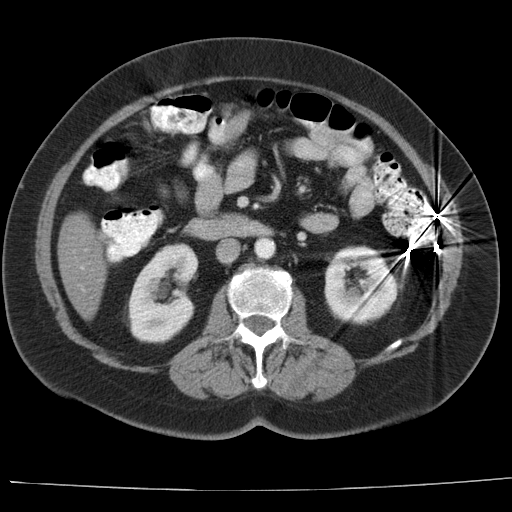
Contrast-enhanced abdominal CT, one axial slice. Position 6 of 44 along the scan axis. Reconstruction kernel AA-1. 140 kVp. Intravenous contrast given. Soft-tissue window (W 400 / L 40 HU). 5 mm slice thickness. 512 × 512 image matrix, field of view 373 × 373 mm. Female patient. From the clinical record (not read from this slice): diagnosis: colorectal cancer liver metastases, imaged before liver resection; multiple liver metastases: yes; largest metastasis: 1.8 cm; chemotherapy before resection: yes.
Structures marked on this image (outlined manually by an expert reader):
- hepatic veins: box from (x=80, y=267) to (x=83, y=270) px
- liver: (x=59, y=213)–(x=107, y=318)
- portal vein (with intrahepatic branches): (x=81, y=288)–(x=84, y=291)